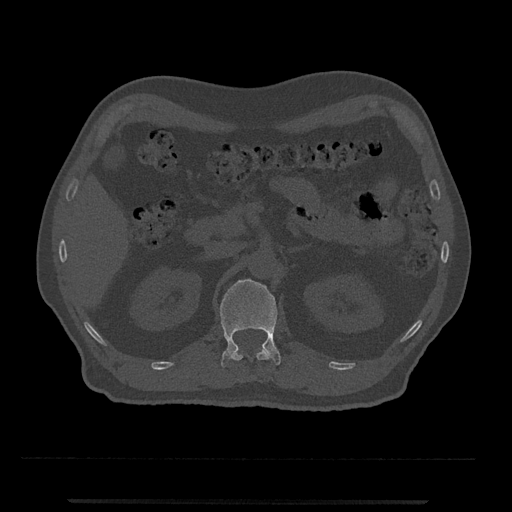
CT including the spine, one axial slice; slice 359 of 797 in the series (ordered by position); 120 kVp; bone window (W 1800 / L 400 HU); 0.5 mm slice thickness; 512 × 512 image matrix, field of view 419 × 419 mm. Male patient, age 63 years. Case-level facts recorded for this patient, not image findings: primary cancer: prostate.
Annotated regions visible in this slice (semi-automatically segmented with operator editing):
- L1 vertebra: bounding box <220,279,281,367> (left, top, right, bottom; pixels)
- T12 vertebra: <232,346,271,361>